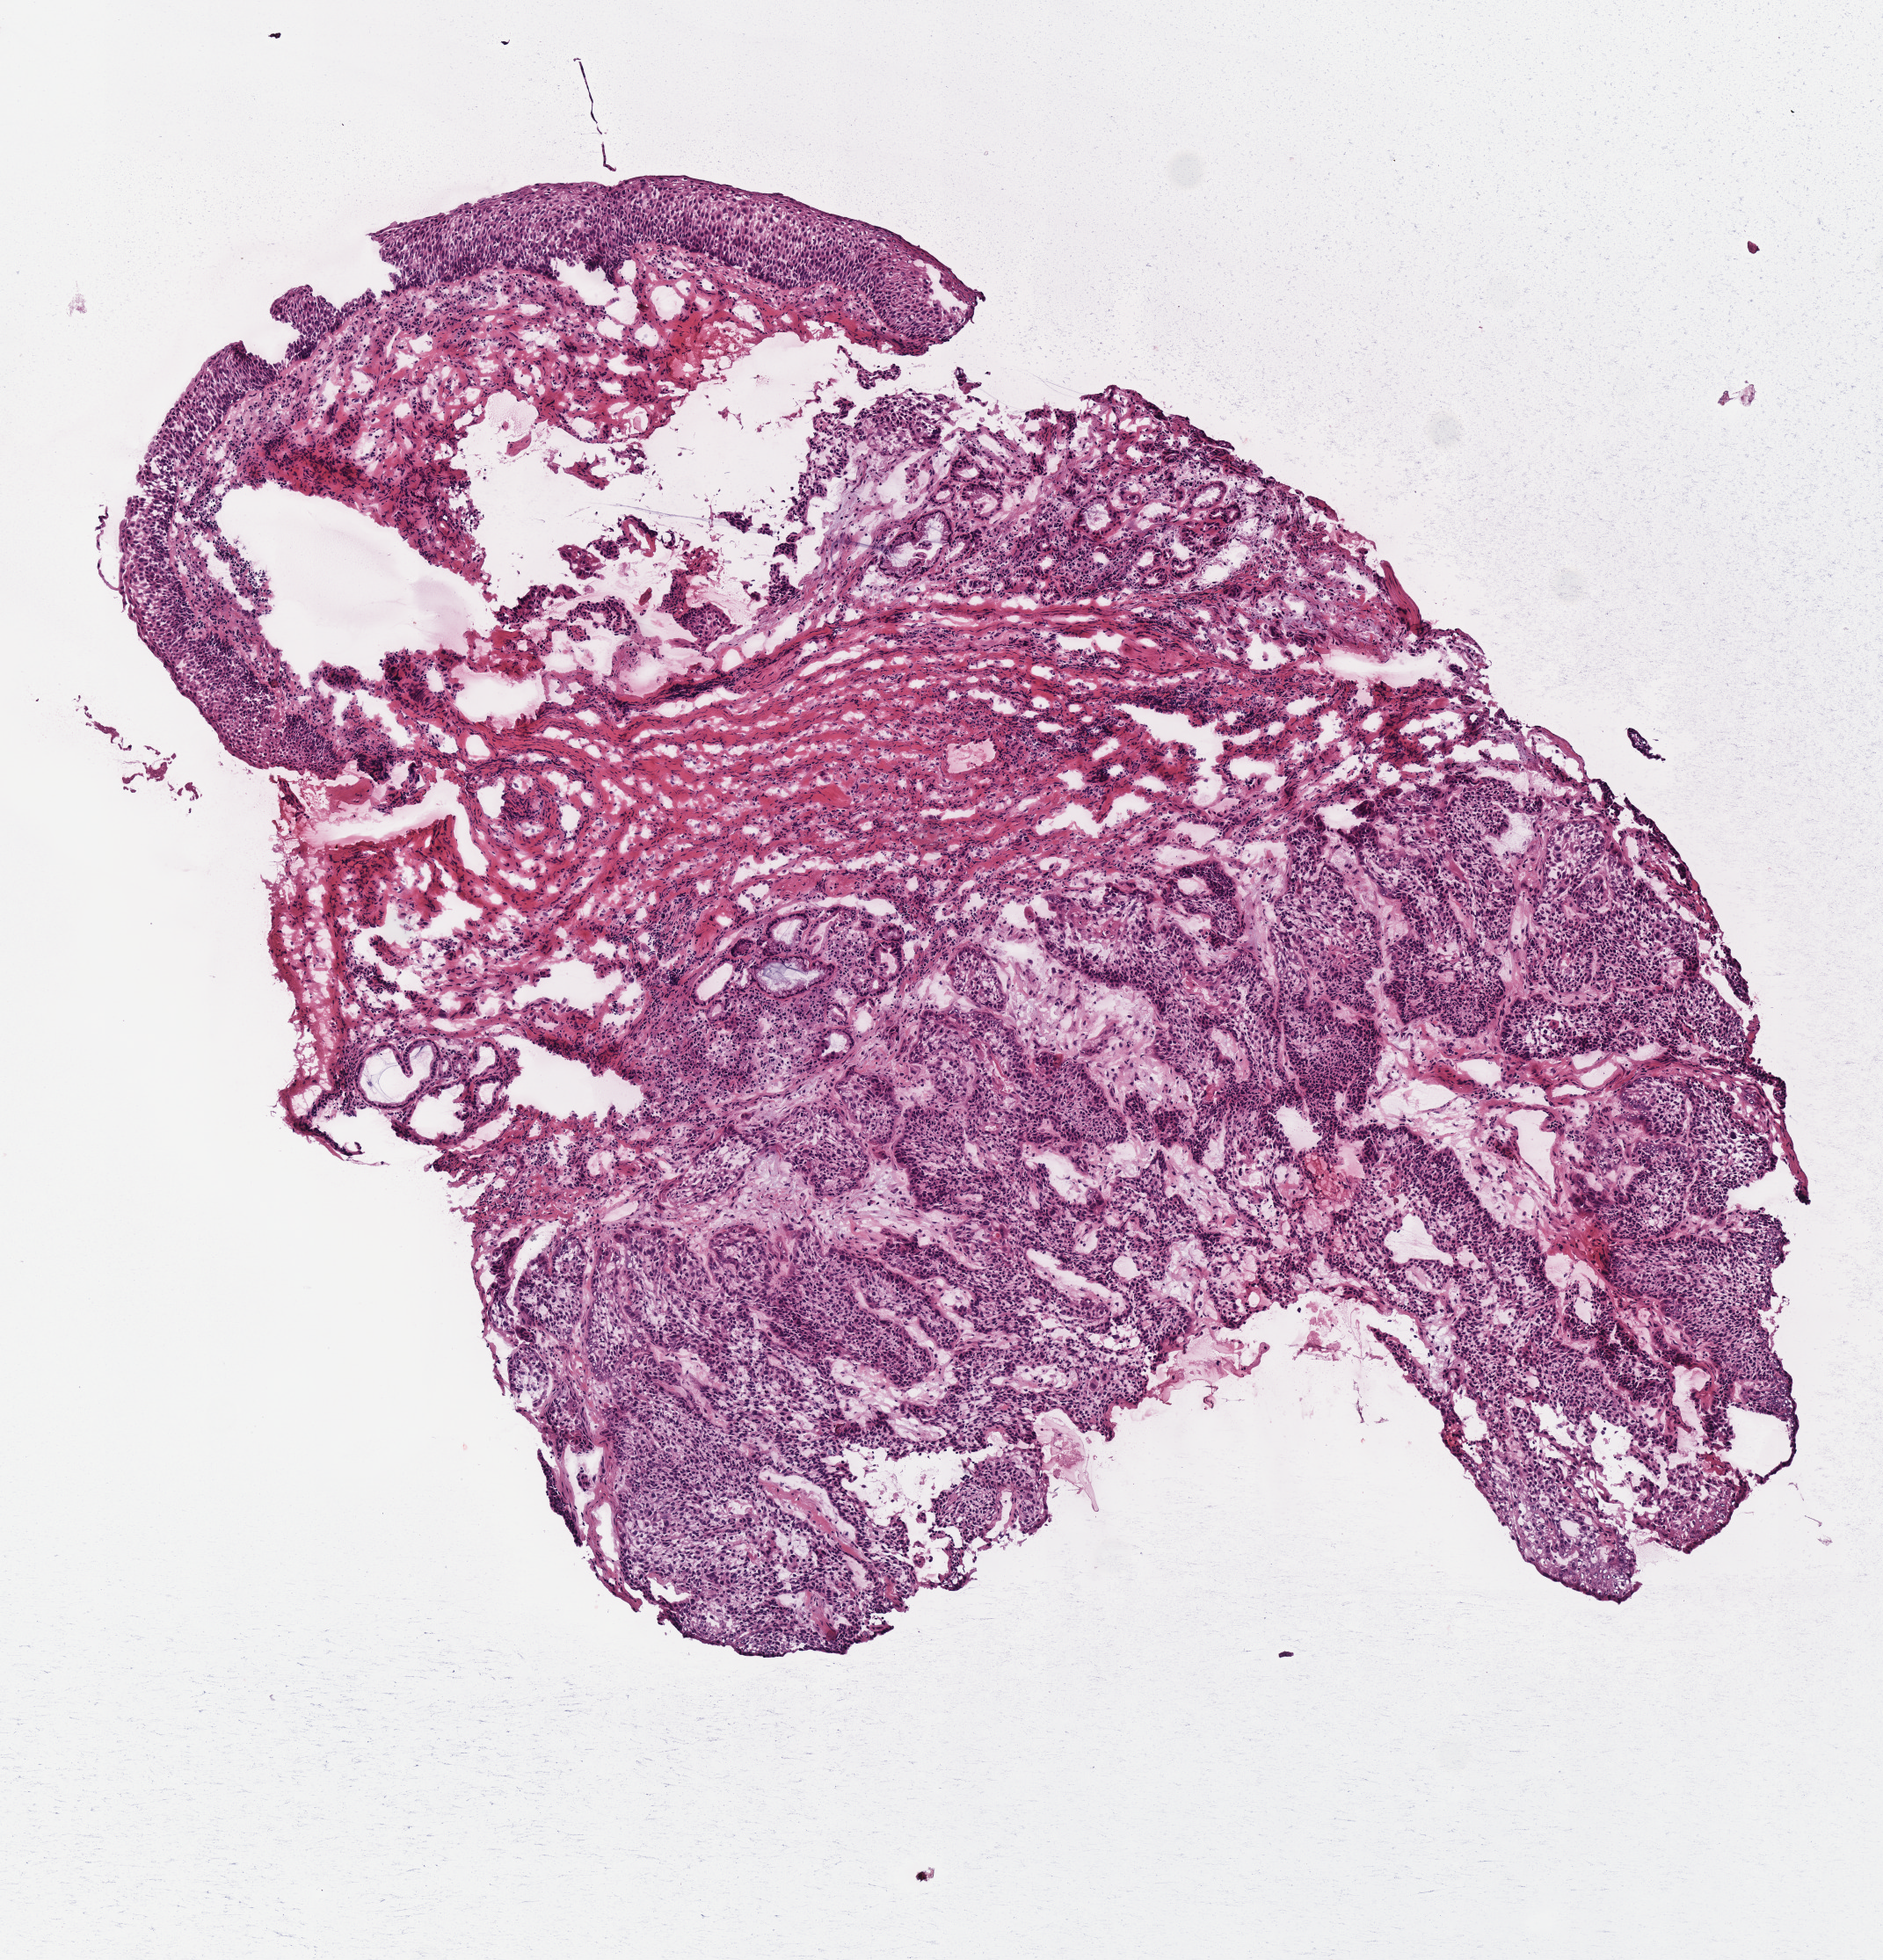
Digitized Hematoxylin and eosin (H&E) stained tissue section (whole slide), low-resolution overview of the scanned area, about 4.2 x 4.4 mm; frozen section from the top of the tissue portion; sample: primary tumour, head and neck. Patient: male, age at initial diagnosis 53 years. Histologic grade: G3 (poorly differentiated). Pathologist review of this section (percent, as recorded): tumour cells 50%, tumour nuclei 60%, normal cells 25%, stromal cells 25%, necrosis 0%. Inflammatory infiltration, as recorded: lymphocyte infiltration 10%.
• diagnosis: Squamous cell carcinoma, NOS (larynx, NOS)
• laterality: left